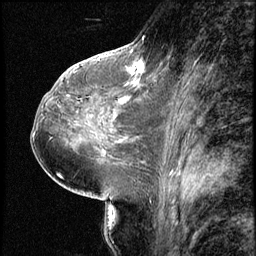
Breast MRI (dynamic contrast-enhanced), one sagittal slice; slice 33 of 66 in the series (ordered by position); 3 images stored at this slice position (order not interpretable as contrast timing); 1.5 T; TE 4.2 ms, TR 8.7 ms; 256 × 256 image matrix. Patient: female, 38 years. From the clinical record (not read from this slice): setting: breast cancer imaged before/during neoadjuvant chemotherapy; receptor status: triple-negative.
Structures marked on this image (semi-automatic segmentation, software-assisted and operator-edited):
- analysis volume of interest (the breast-tissue region the enhancement analysis was run in; not a lesion): bounding box <128,57,149,78> (left, top, right, bottom; pixels)
- tumour enhancement mask (voxels above the 140 % enhancement threshold inside the analysis volume of interest): <128,62,144,74>